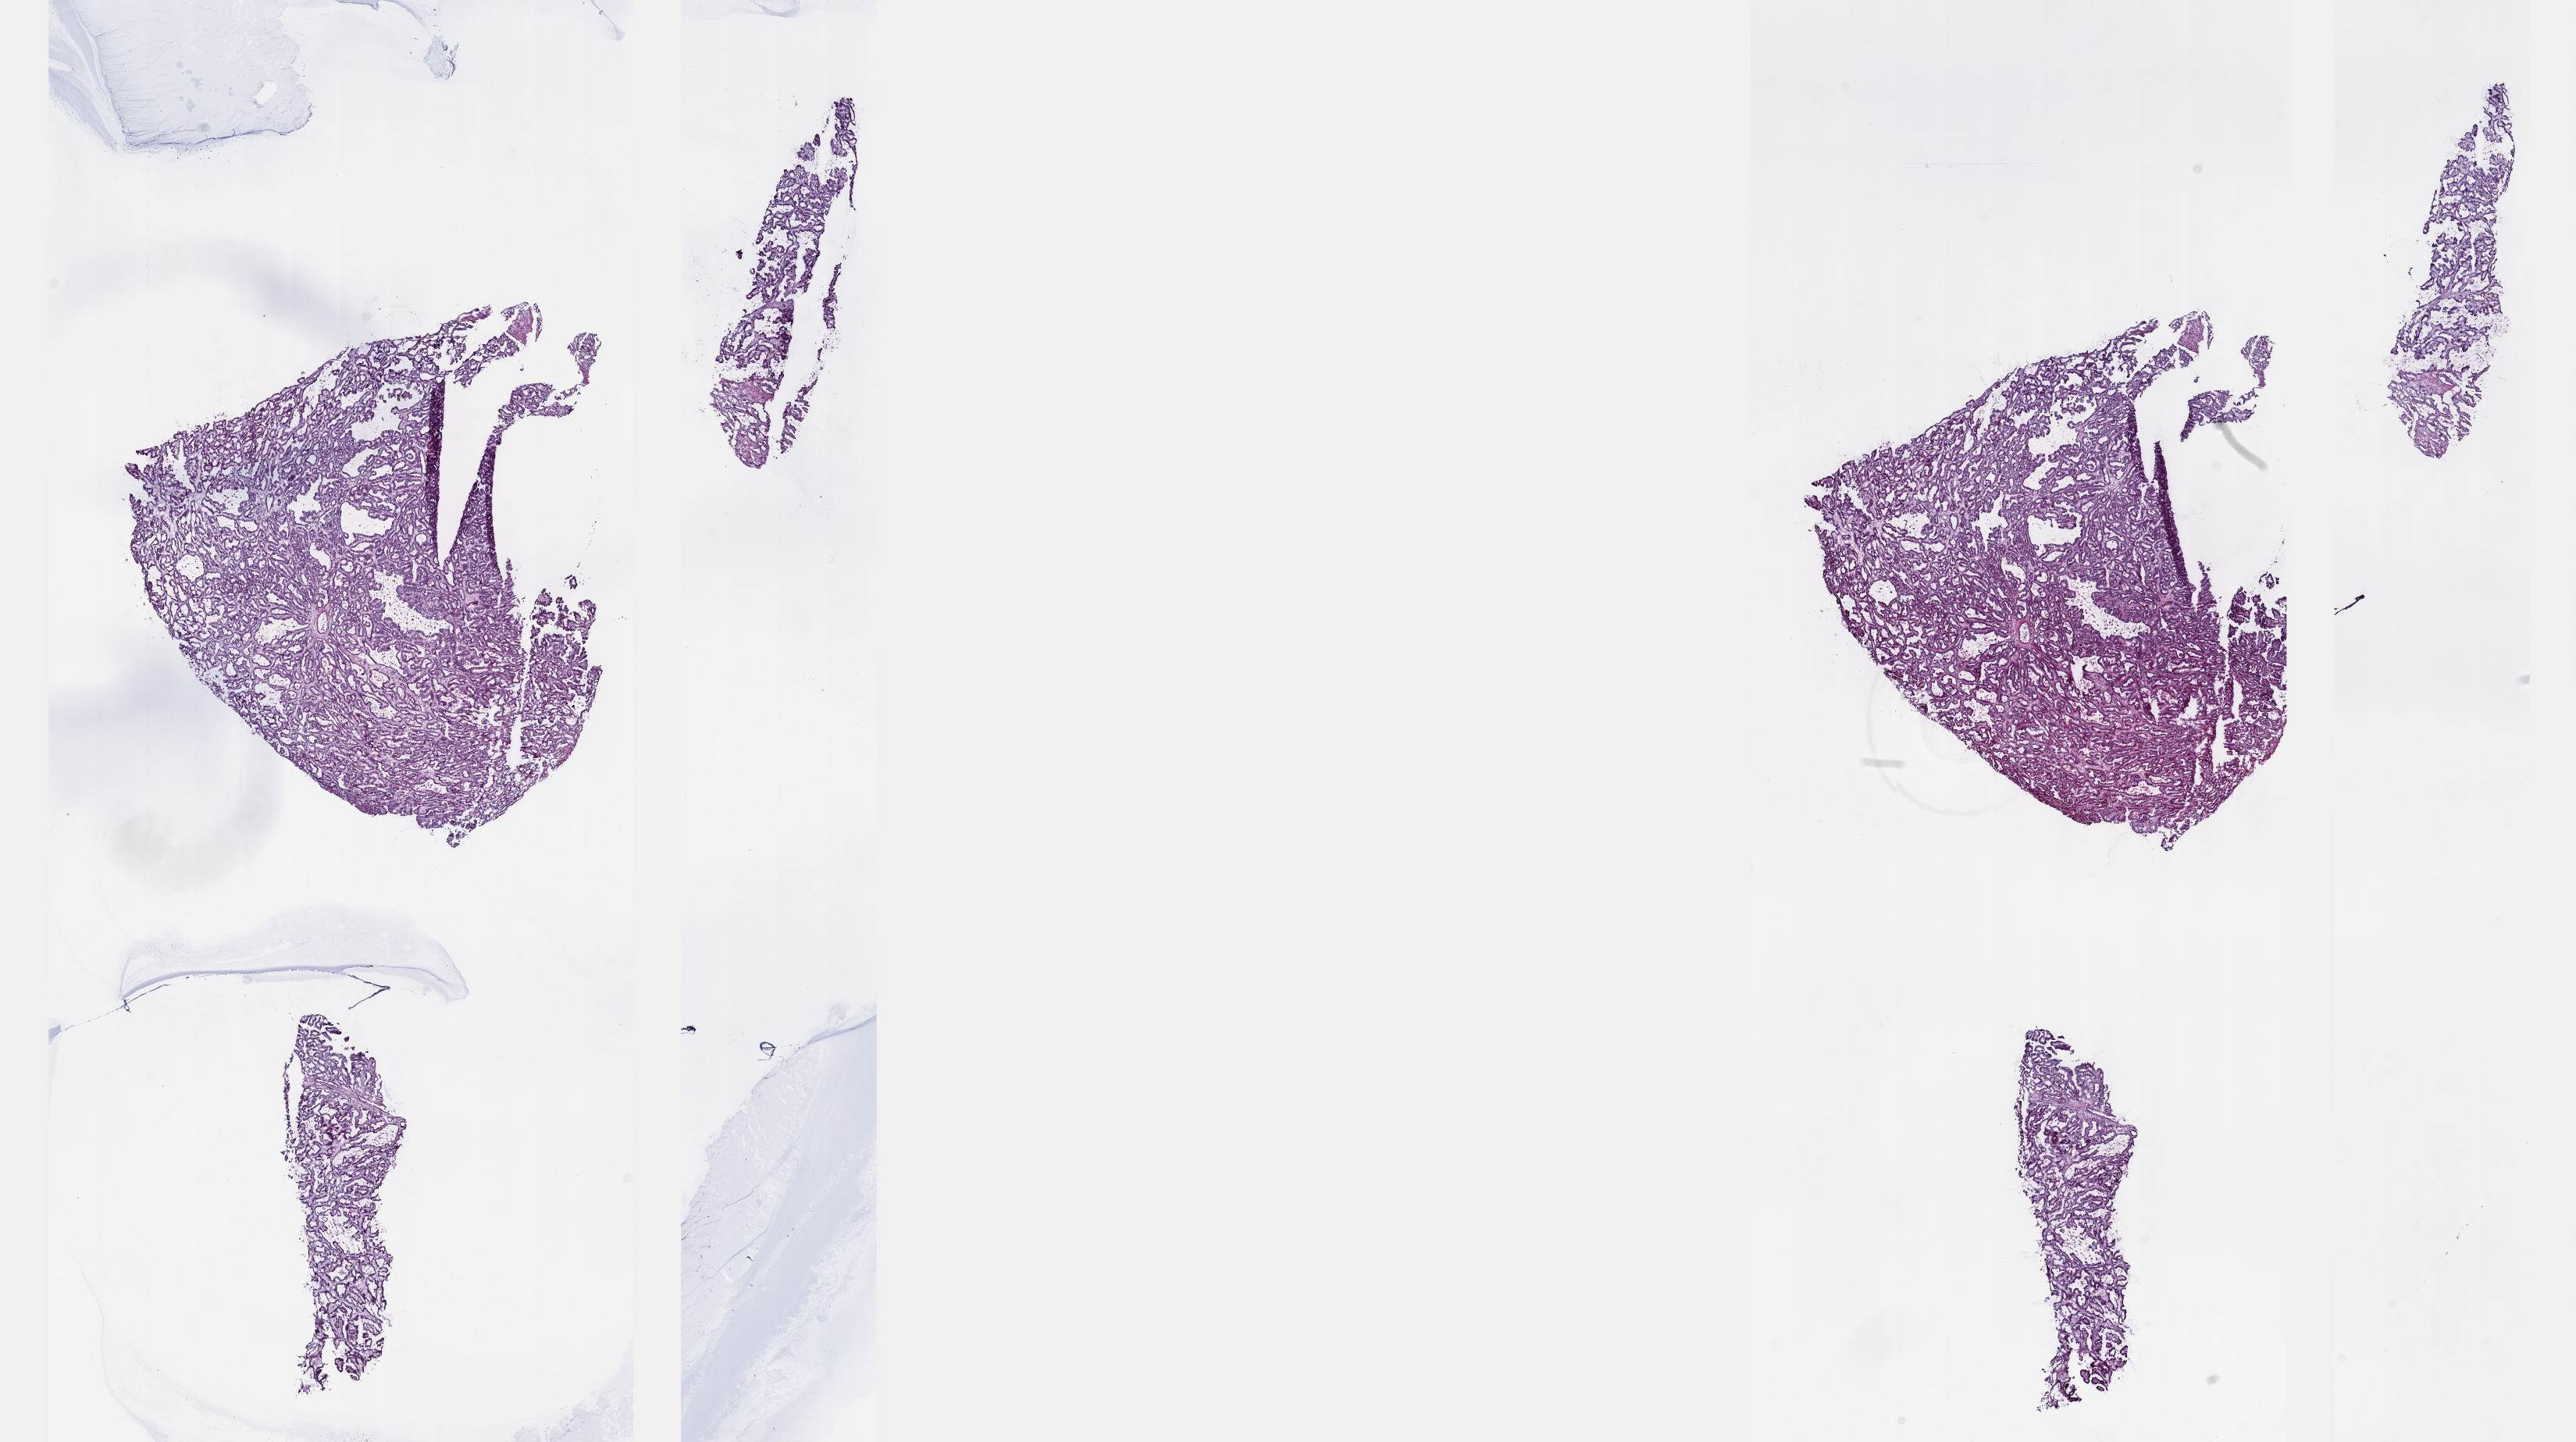
Whole-slide histology image, H&E-stained, low-resolution overview of the scanned area, about 26.7 x 14.9 mm, frozen section from the top of the tissue portion, primary tumour sample from the kidney. Patient: female, age at initial diagnosis 50 years. Composition of this section per pathologist review: tumour cells 100%, tumour nuclei 80%.
Histologic diagnosis: Papillary adenocarcinoma, NOS.